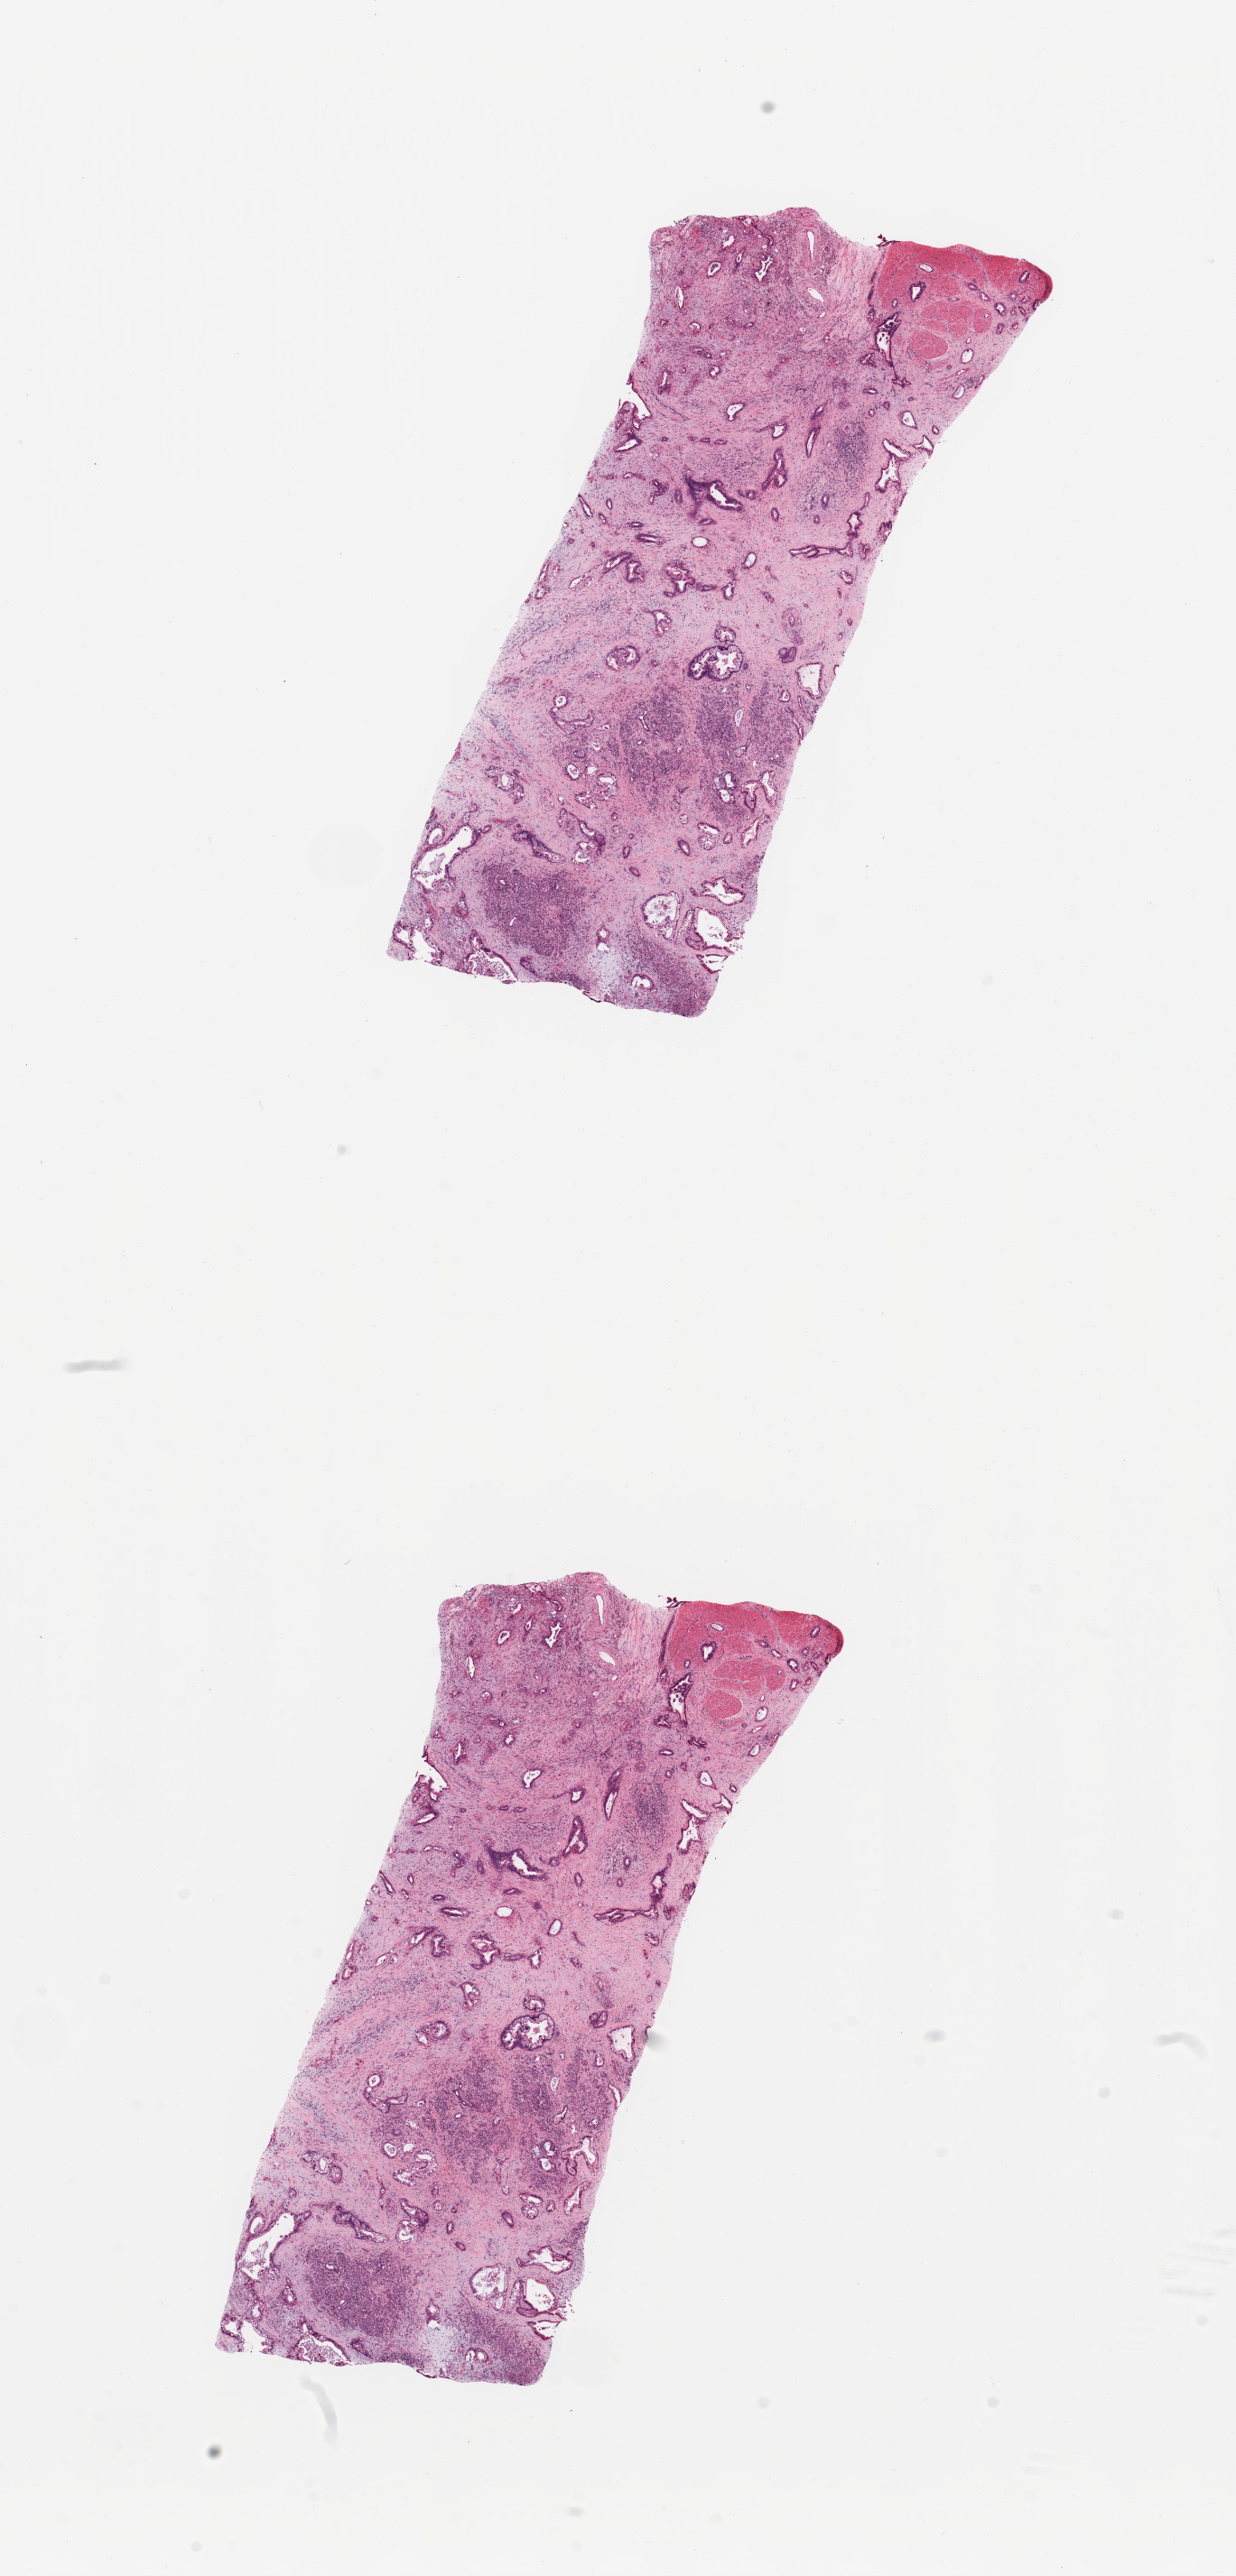
Whole-slide histology image, H&E — low-resolution overview of the scanned area, about 10.8 x 22.6 mm; tumour tissue sample, sampled site: pancreas. Male, 80 y/o.
Diagnosis: Infiltrating duct carcinoma, NOS.